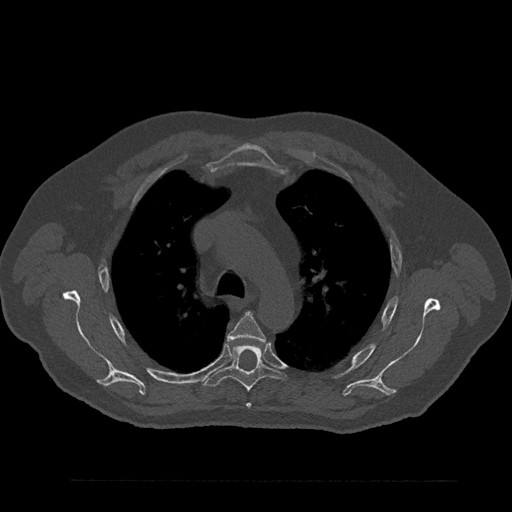
CT including the spine, one axial slice. Position 614 of 797 along the scan axis. Reconstruction kernel Br40s/3. Bone window (W 1800 / L 400 HU). 512 × 512 image matrix, field of view 430 × 430 mm. Patient: male, 61 years. From the clinical record (not read from this slice): primary cancer: prostate.
Structures marked on this image (semi-automatically segmented with operator editing):
- T4 vertebra: bounding box (x1, y1, x2, y2) in pixels: (227, 313, 266, 408)
- T5 vertebra: (204, 344, 286, 392)